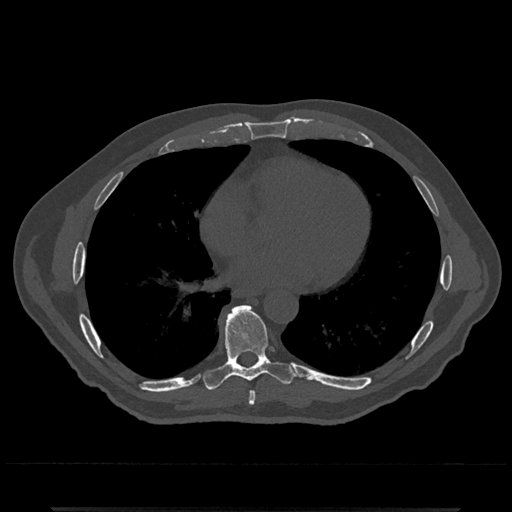
CT including the spine, one axial slice; position 673 of 797 along the scan axis; reconstruction kernel Br40s/3; 120 kVp; bone window (W 1800 / L 400 HU); 0.5 mm slice thickness; 512 × 512 image matrix, field of view 393 × 393 mm. Patient: male, 67 years. Case-level facts recorded for this patient, not image findings: primary cancer: prostate.
Outlined on this slice (semi-automatically segmented with operator editing):
- T7 vertebra: box from (x=248, y=391) to (x=256, y=406) px
- T8 vertebra: (x=203, y=305)–(x=295, y=390)